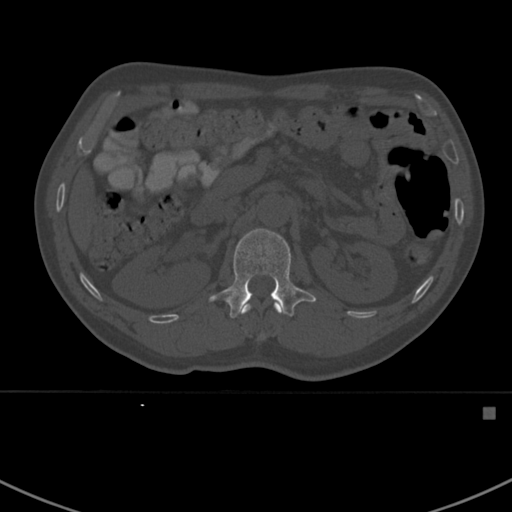
CT including the spine, one axial slice; position 313 of 412 along the scan axis; reconstruction kernel Br40s; 120 kVp; bone window (W 1800 / L 400 HU); 1.5 mm slice thickness; 512 × 512 image matrix, field of view 358 × 358 mm. Male patient, age 59 years. Case-level facts recorded for this patient, not image findings: primary cancer: prostate.
Annotated regions visible in this slice (semi-automatically segmented with operator editing):
- L1 vertebra: box from (x=208, y=228) to (x=316, y=318) px
- T12 vertebra: (x=242, y=303)–(x=281, y=341)